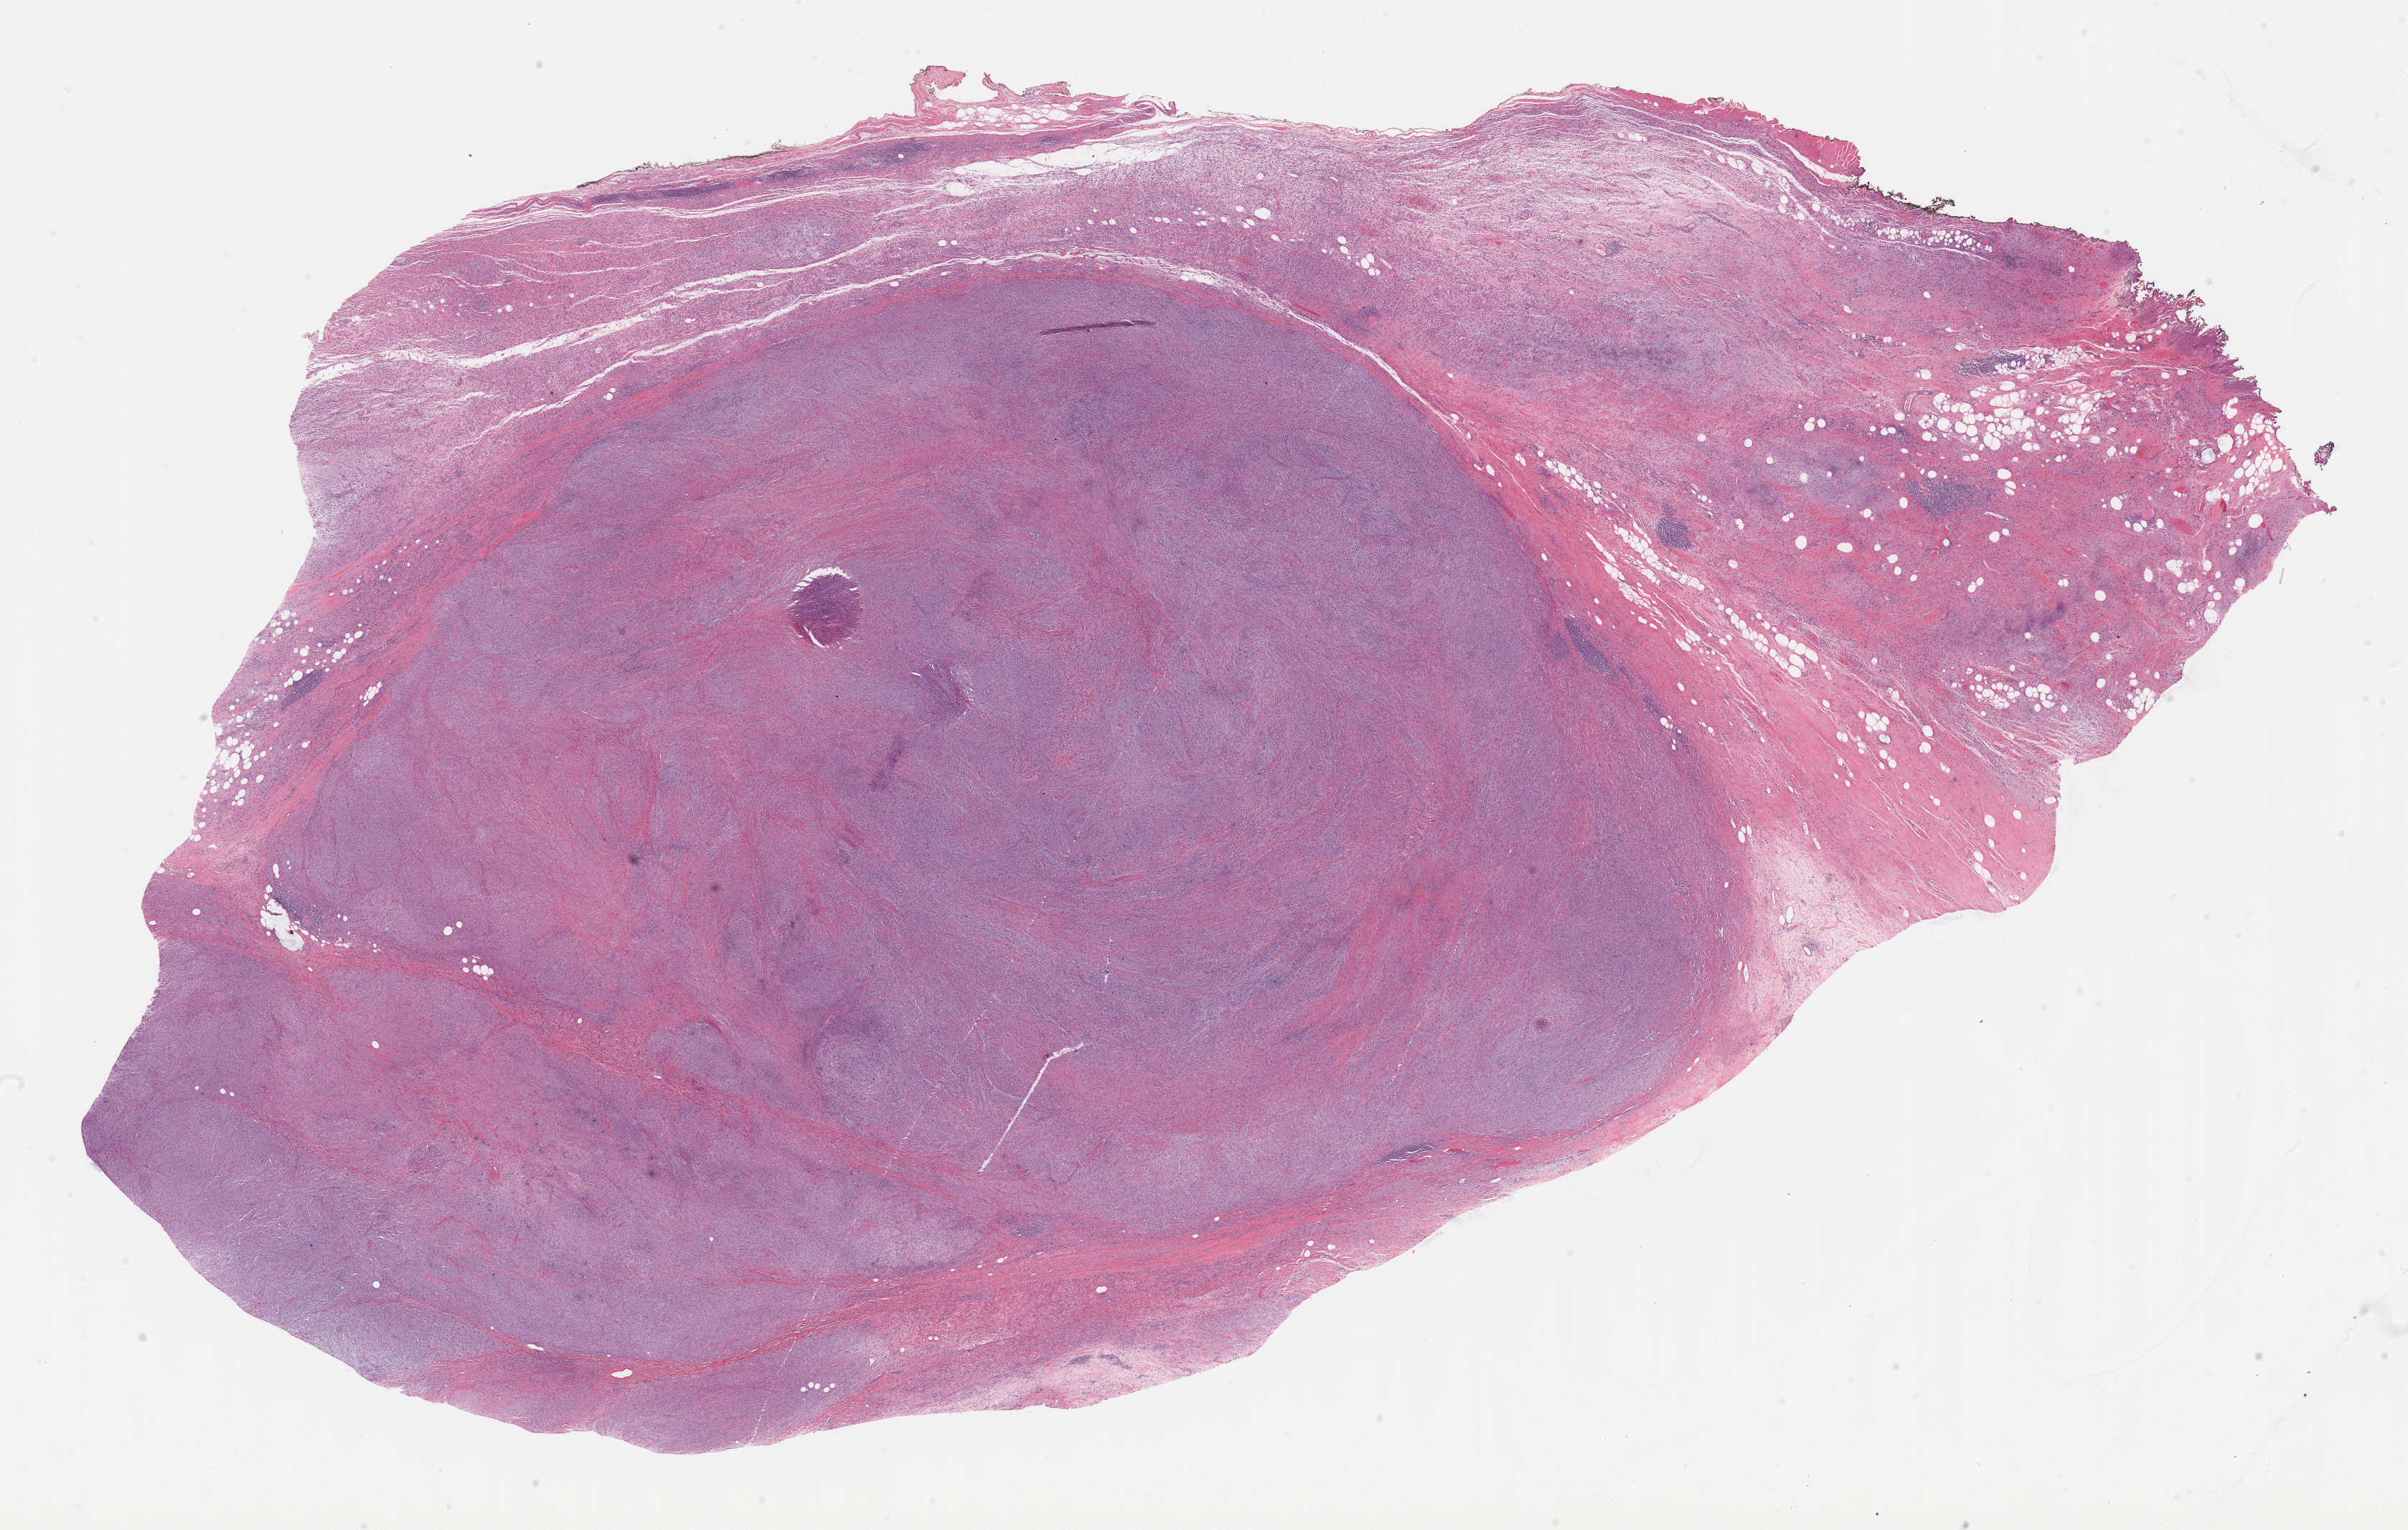
Digitized H&E tissue section (whole slide) — a low-resolution overview of the entire scanned area, about 26.7 x 17.0 mm (from a 20x scan); FFPE section; primary tumour sample from the retroperitoneum and peritoneum. Female, age 85 years at initial diagnosis.
Histologic diagnosis: Dedifferentiated liposarcoma (retroperitoneum).